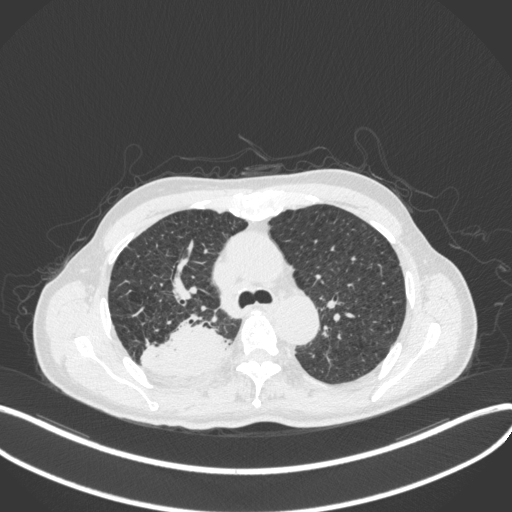
Chest CT, one axial slice; position 311 of 423 along the scan axis; reconstruction kernel B31f; 120 kVp; lung window (W 1500 / L -600 HU); 1 mm slice thickness; 512 × 512 image matrix, field of view 400 × 400 mm. Male patient, age 79 years. Case-level facts recorded for this patient, not image findings: clinical TNM (as recorded): T3 N0 M0.
Annotated regions visible in this slice (rectangle marked by the reading radiologist):
- lung tumour (recorded histology: adenocarcinoma): box from (x=142, y=312) to (x=230, y=379) px